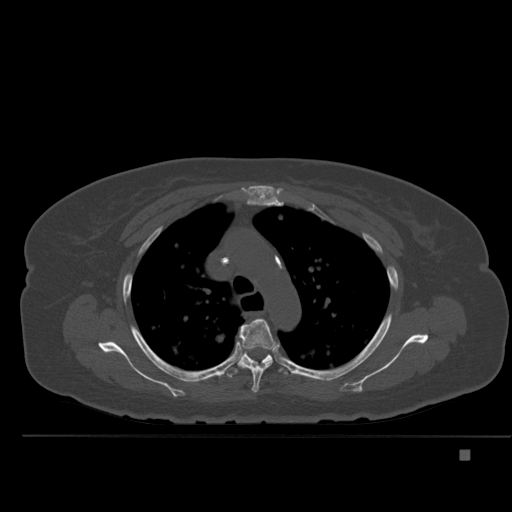
CT including the spine, one axial slice. Position 362 of 477 along the scan axis. Bone window (W 1800 / L 400 HU). 1.5 mm slice thickness. 512 × 512 image matrix, field of view 422 × 422 mm. Female patient, age 74 years. Case-level facts recorded for this patient, not image findings: primary cancer: colon.
Outlined on this slice (semi-automatic segmentation, software-assisted and operator-edited):
- T4 vertebra: bounding box (x1, y1, x2, y2) in pixels: (238, 318, 278, 393)
- T5 vertebra: (227, 337, 288, 378)